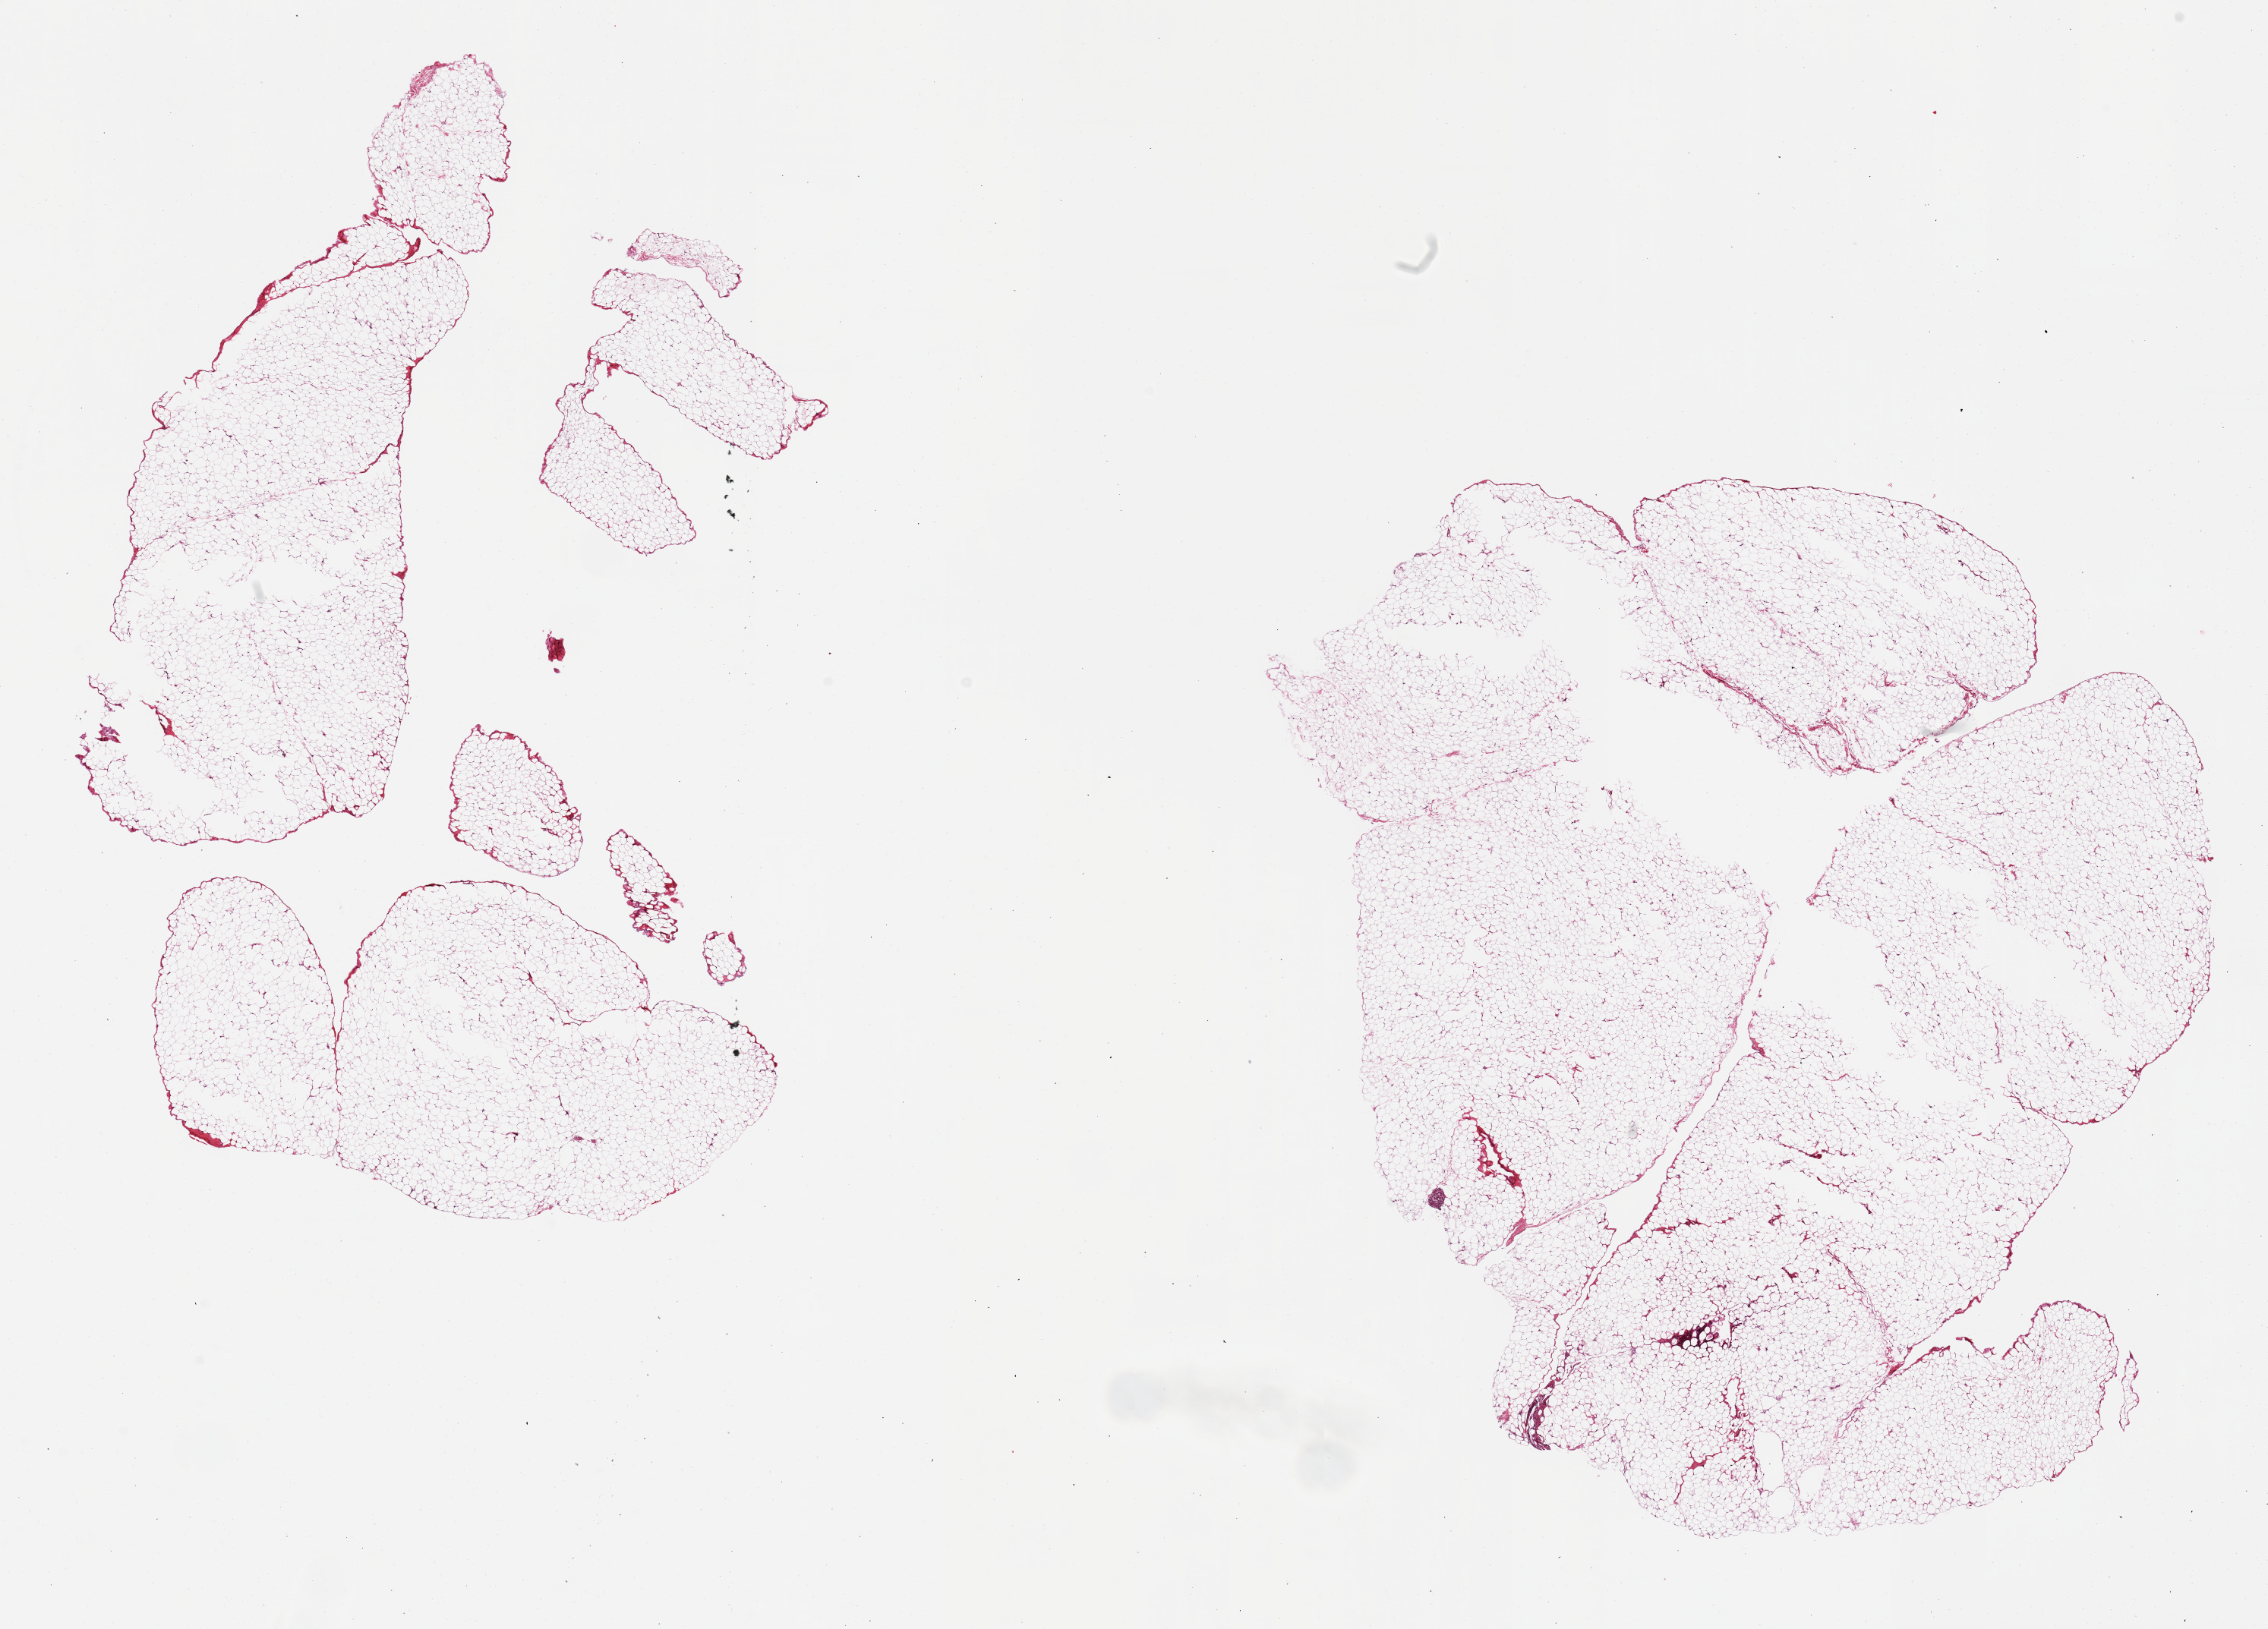
Whole-slide image, hematoxylin and eosin (H&E) stain — shown as a low-resolution overview of the whole scanned area (about 23.6 x 17.0 mm). PAXgene-fixed paraffin-embedded (PFPE) section. Section of omentum (target tissue). Donor tissue sample. Female donor.
Pathologist's review note for this sample: 2 pieces, no abnormalities.